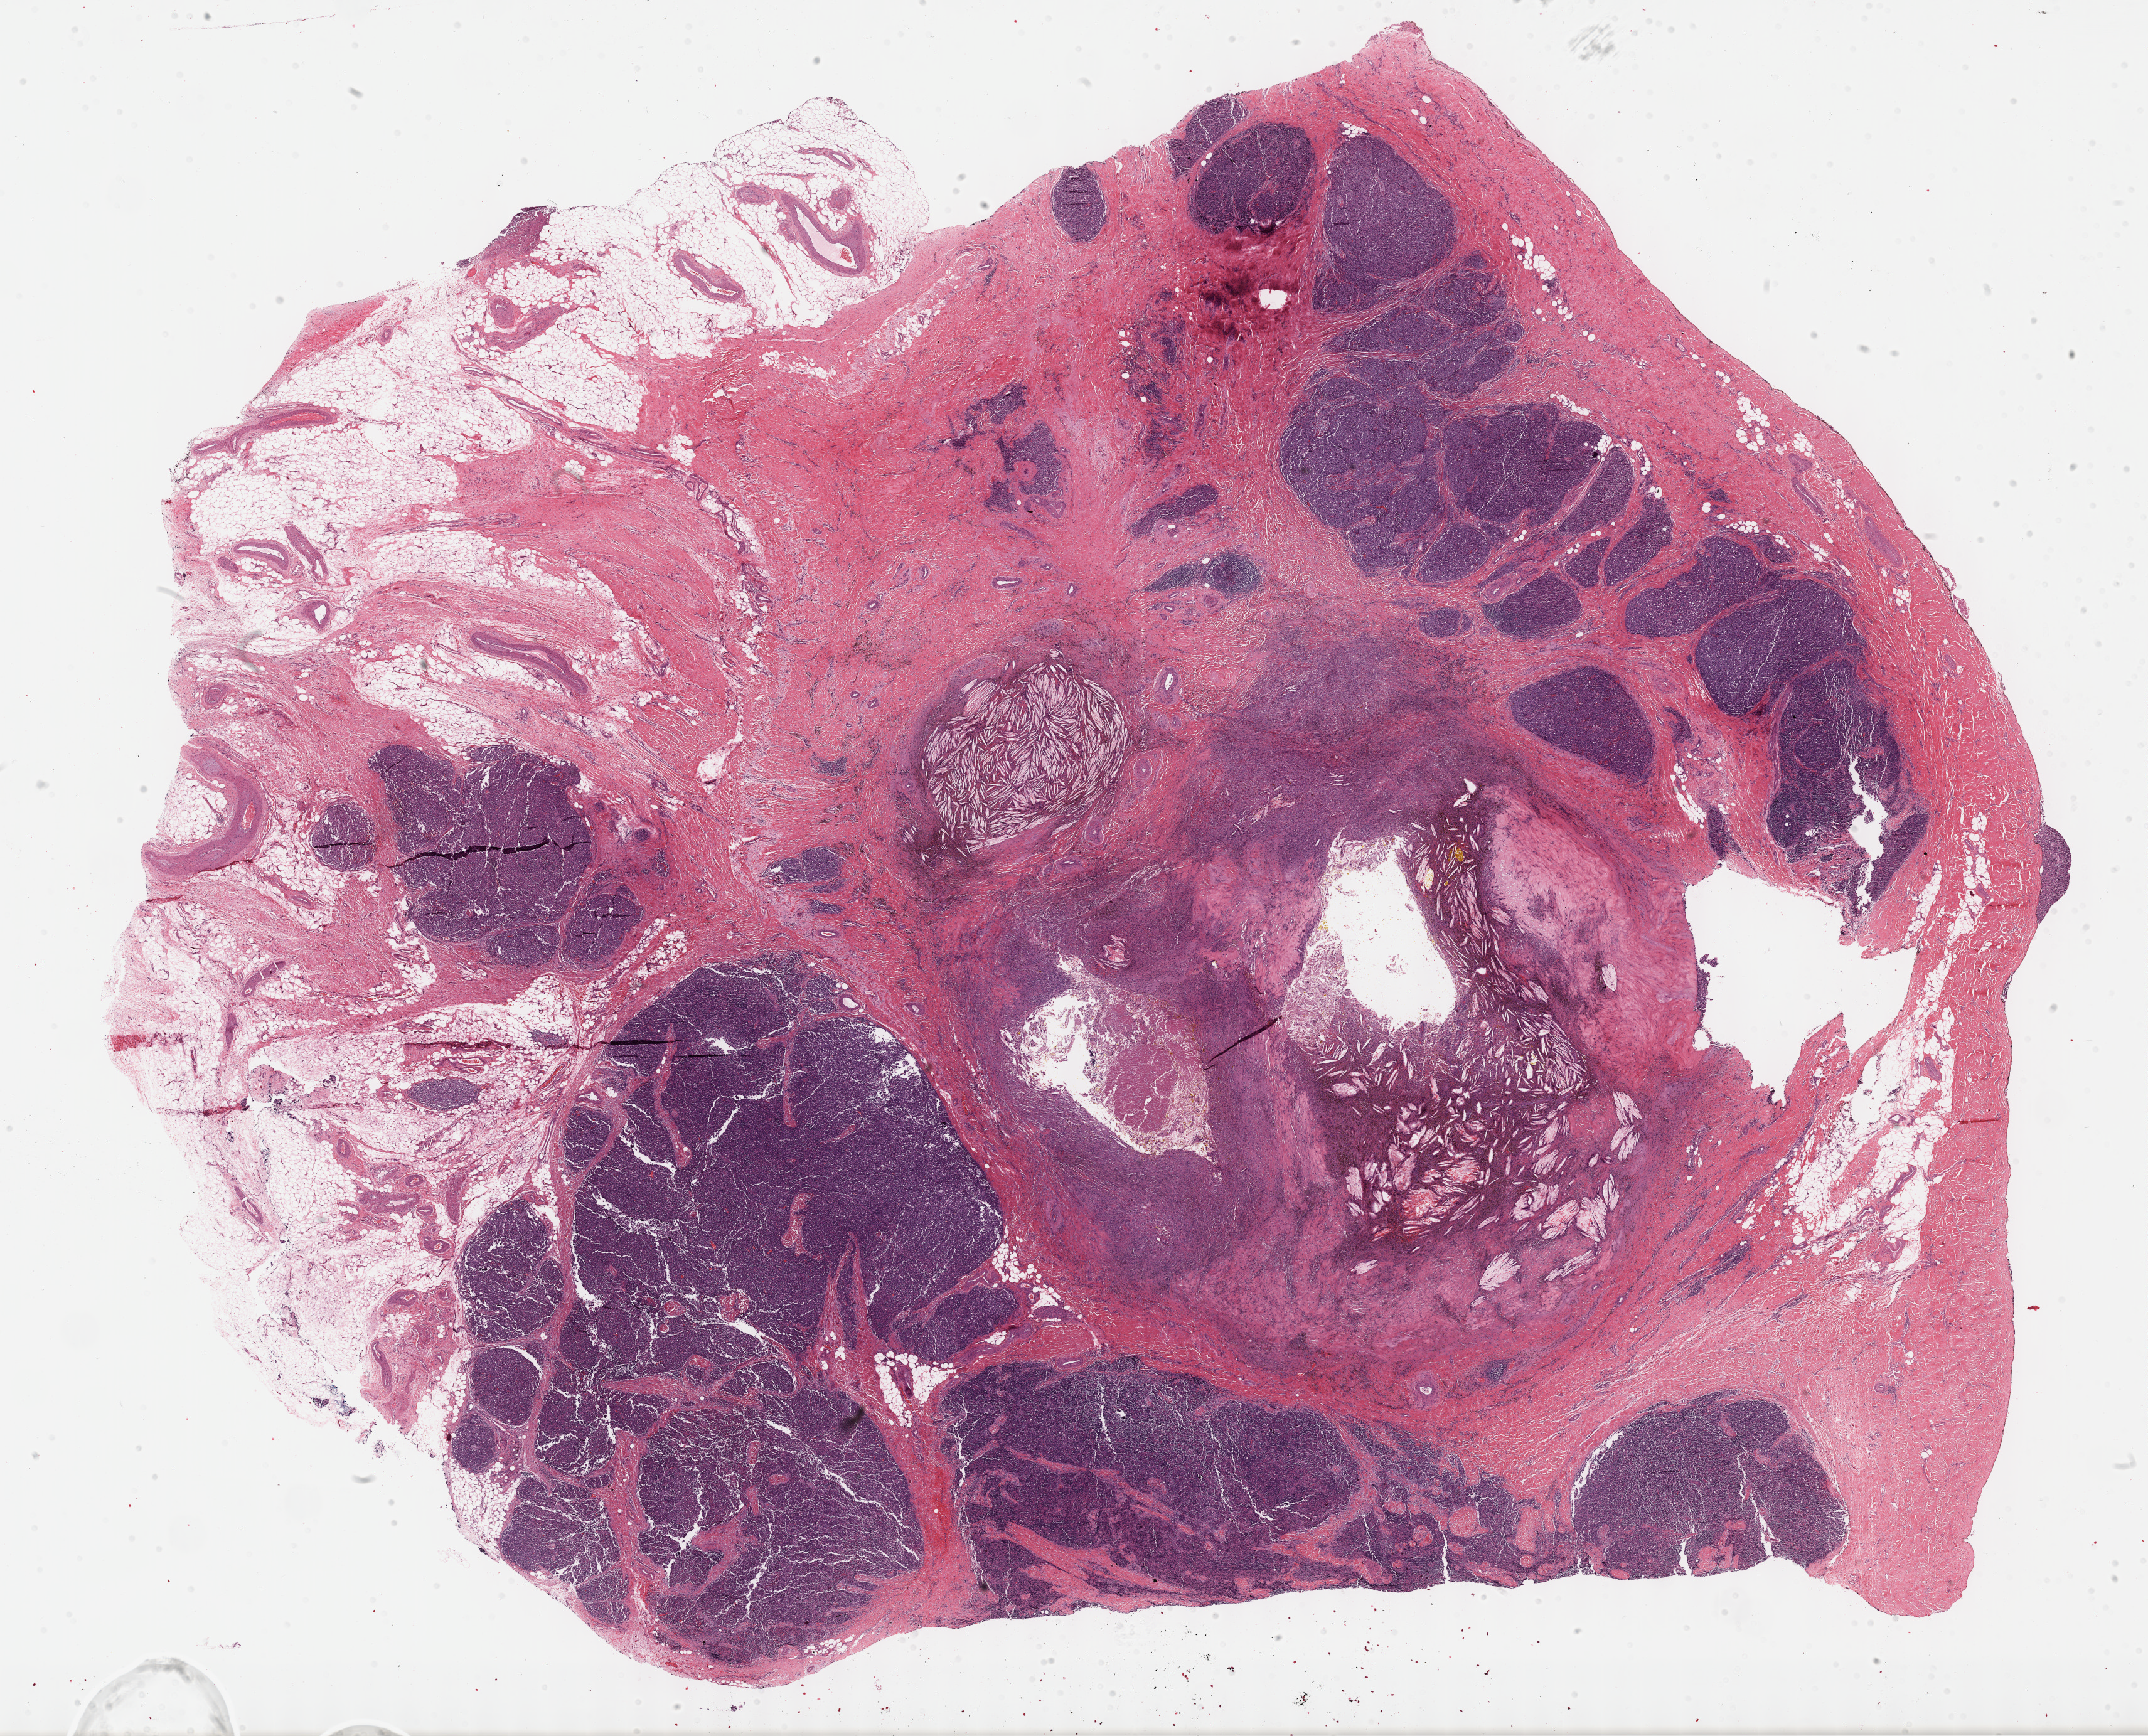
H&E-stained whole-slide image, whole scanned area (about 27.7 x 22.4 mm) shown as a low-resolution overview; FFPE section; thymus, primary tumour sample. Male, age 67 years at initial diagnosis.
Diagnosis: Thymoma, type B2, malignant (anterior mediastinum).